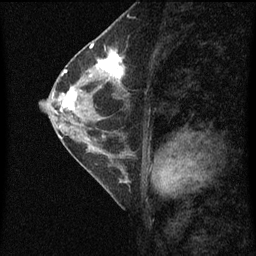
Breast MRI (dynamic contrast-enhanced), one sagittal slice. Slice 33 of 60 in the series (ordered by position). Dynamic contrast-enhanced series, image 2 of 4 at this slice position (ordered by acquisition). 1.5 T. TE 4.2 ms, TR 8 ms. 2 mm slice thickness. 256 × 256 image matrix, field of view 180 × 180 mm. Female patient, age 56 years.
Structures marked on this image (semi-automatic segmentation, software-assisted and operator-edited):
- analysis volume of interest (the breast-tissue region the enhancement analysis was run in; not a lesion): bounding box (x1, y1, x2, y2) in pixels: (56, 52, 127, 115)
- tumour enhancement mask (voxels above the 70 % enhancement threshold inside the analysis volume of interest): (58, 54, 125, 113)